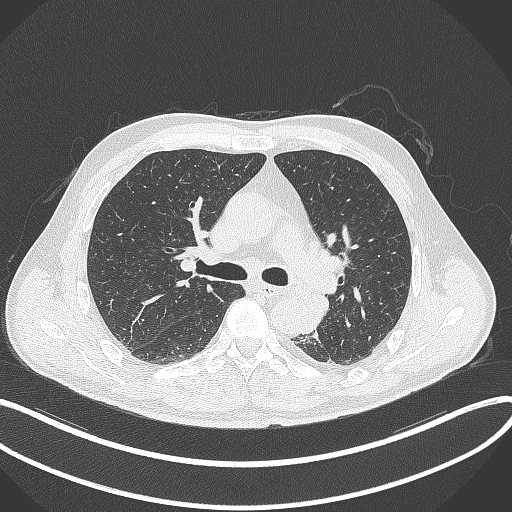
Chest CT, one axial slice. Slice 217 of 329 in the series (ordered by position). Reconstruction kernel B70f. Lung window (W 1500 / L -600 HU). 512 × 512 image matrix. Patient: male, 59 years. From the clinical record (not read from this slice): clinical TNM (as recorded): T2a N2 M0.
Structures marked on this image (rectangle marked by the reading radiologist):
- lung tumour (recorded histology: squamous cell carcinoma): bounding box (x1, y1, x2, y2) in pixels: (302, 290, 330, 326)